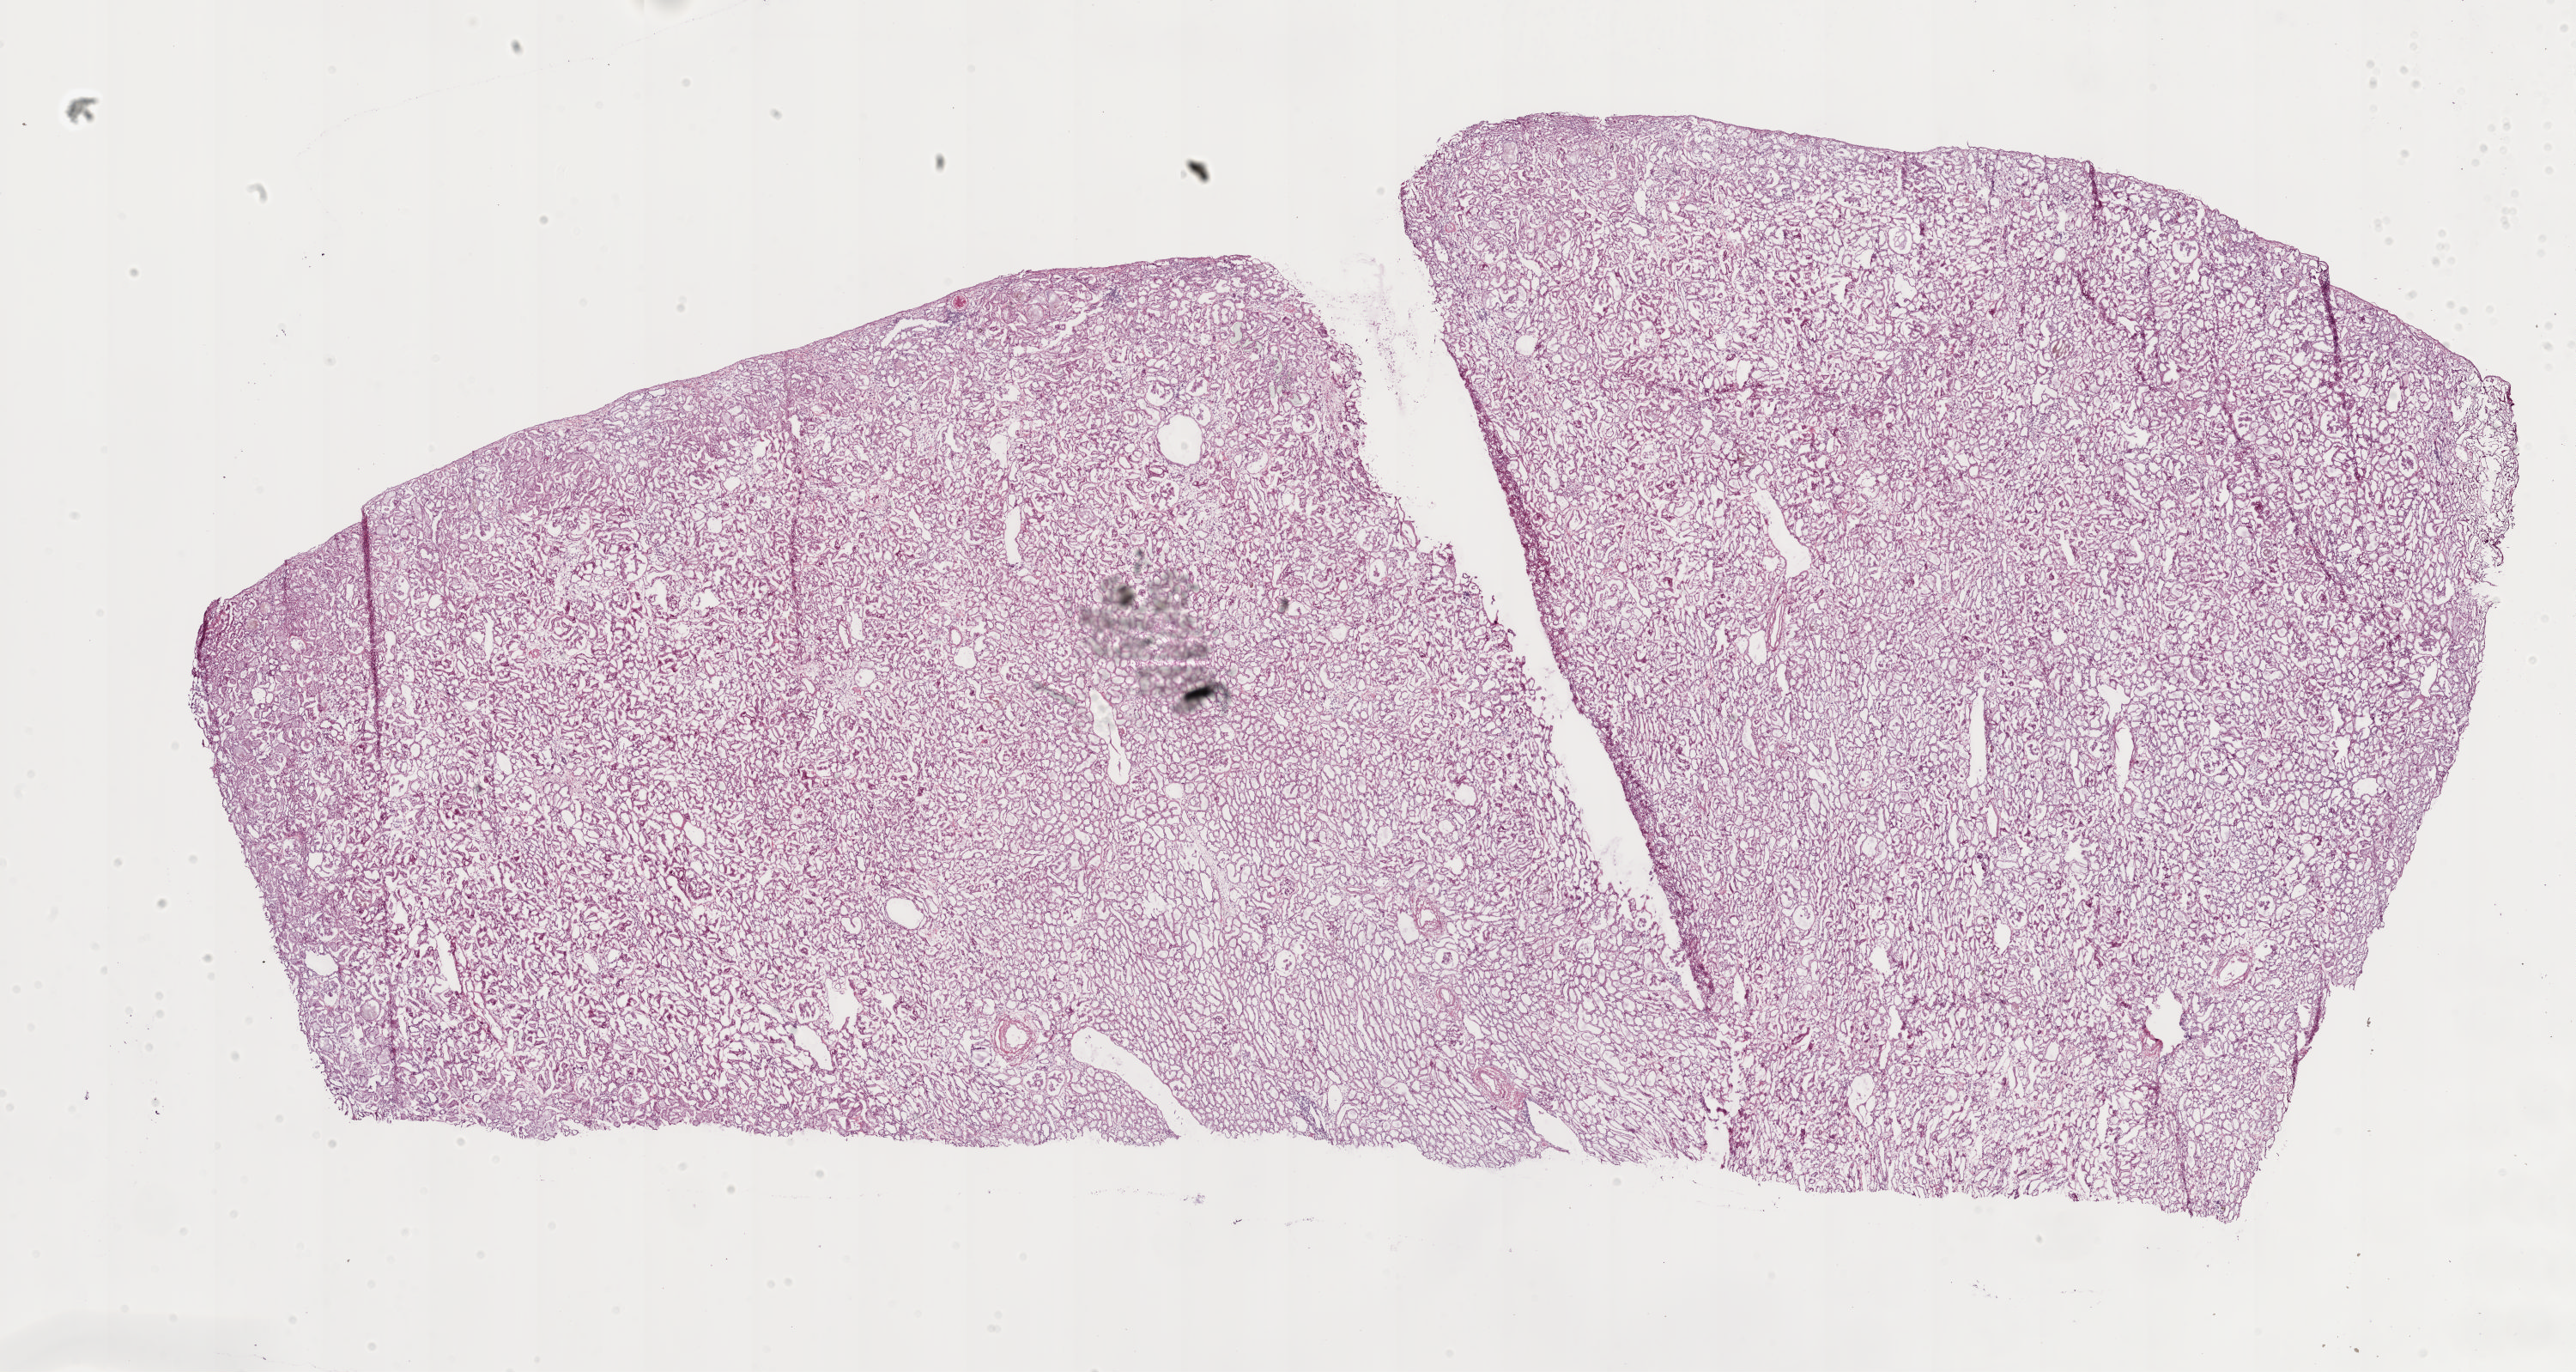
Whole-slide histology image, H&E-stained, whole scanned area (about 23.8 x 12.7 mm, acquisition: 20x scan) shown as a low-resolution overview. Frozen section from the bottom of the tissue portion. Solid tissue normal (non-tumour tissue) sample from the kidney. Patient: male, age at initial diagnosis 58 years.
• this section: solid tissue normal (non-tumour) sample from the same patient
• patient diagnosis: Clear cell adenocarcinoma, NOS